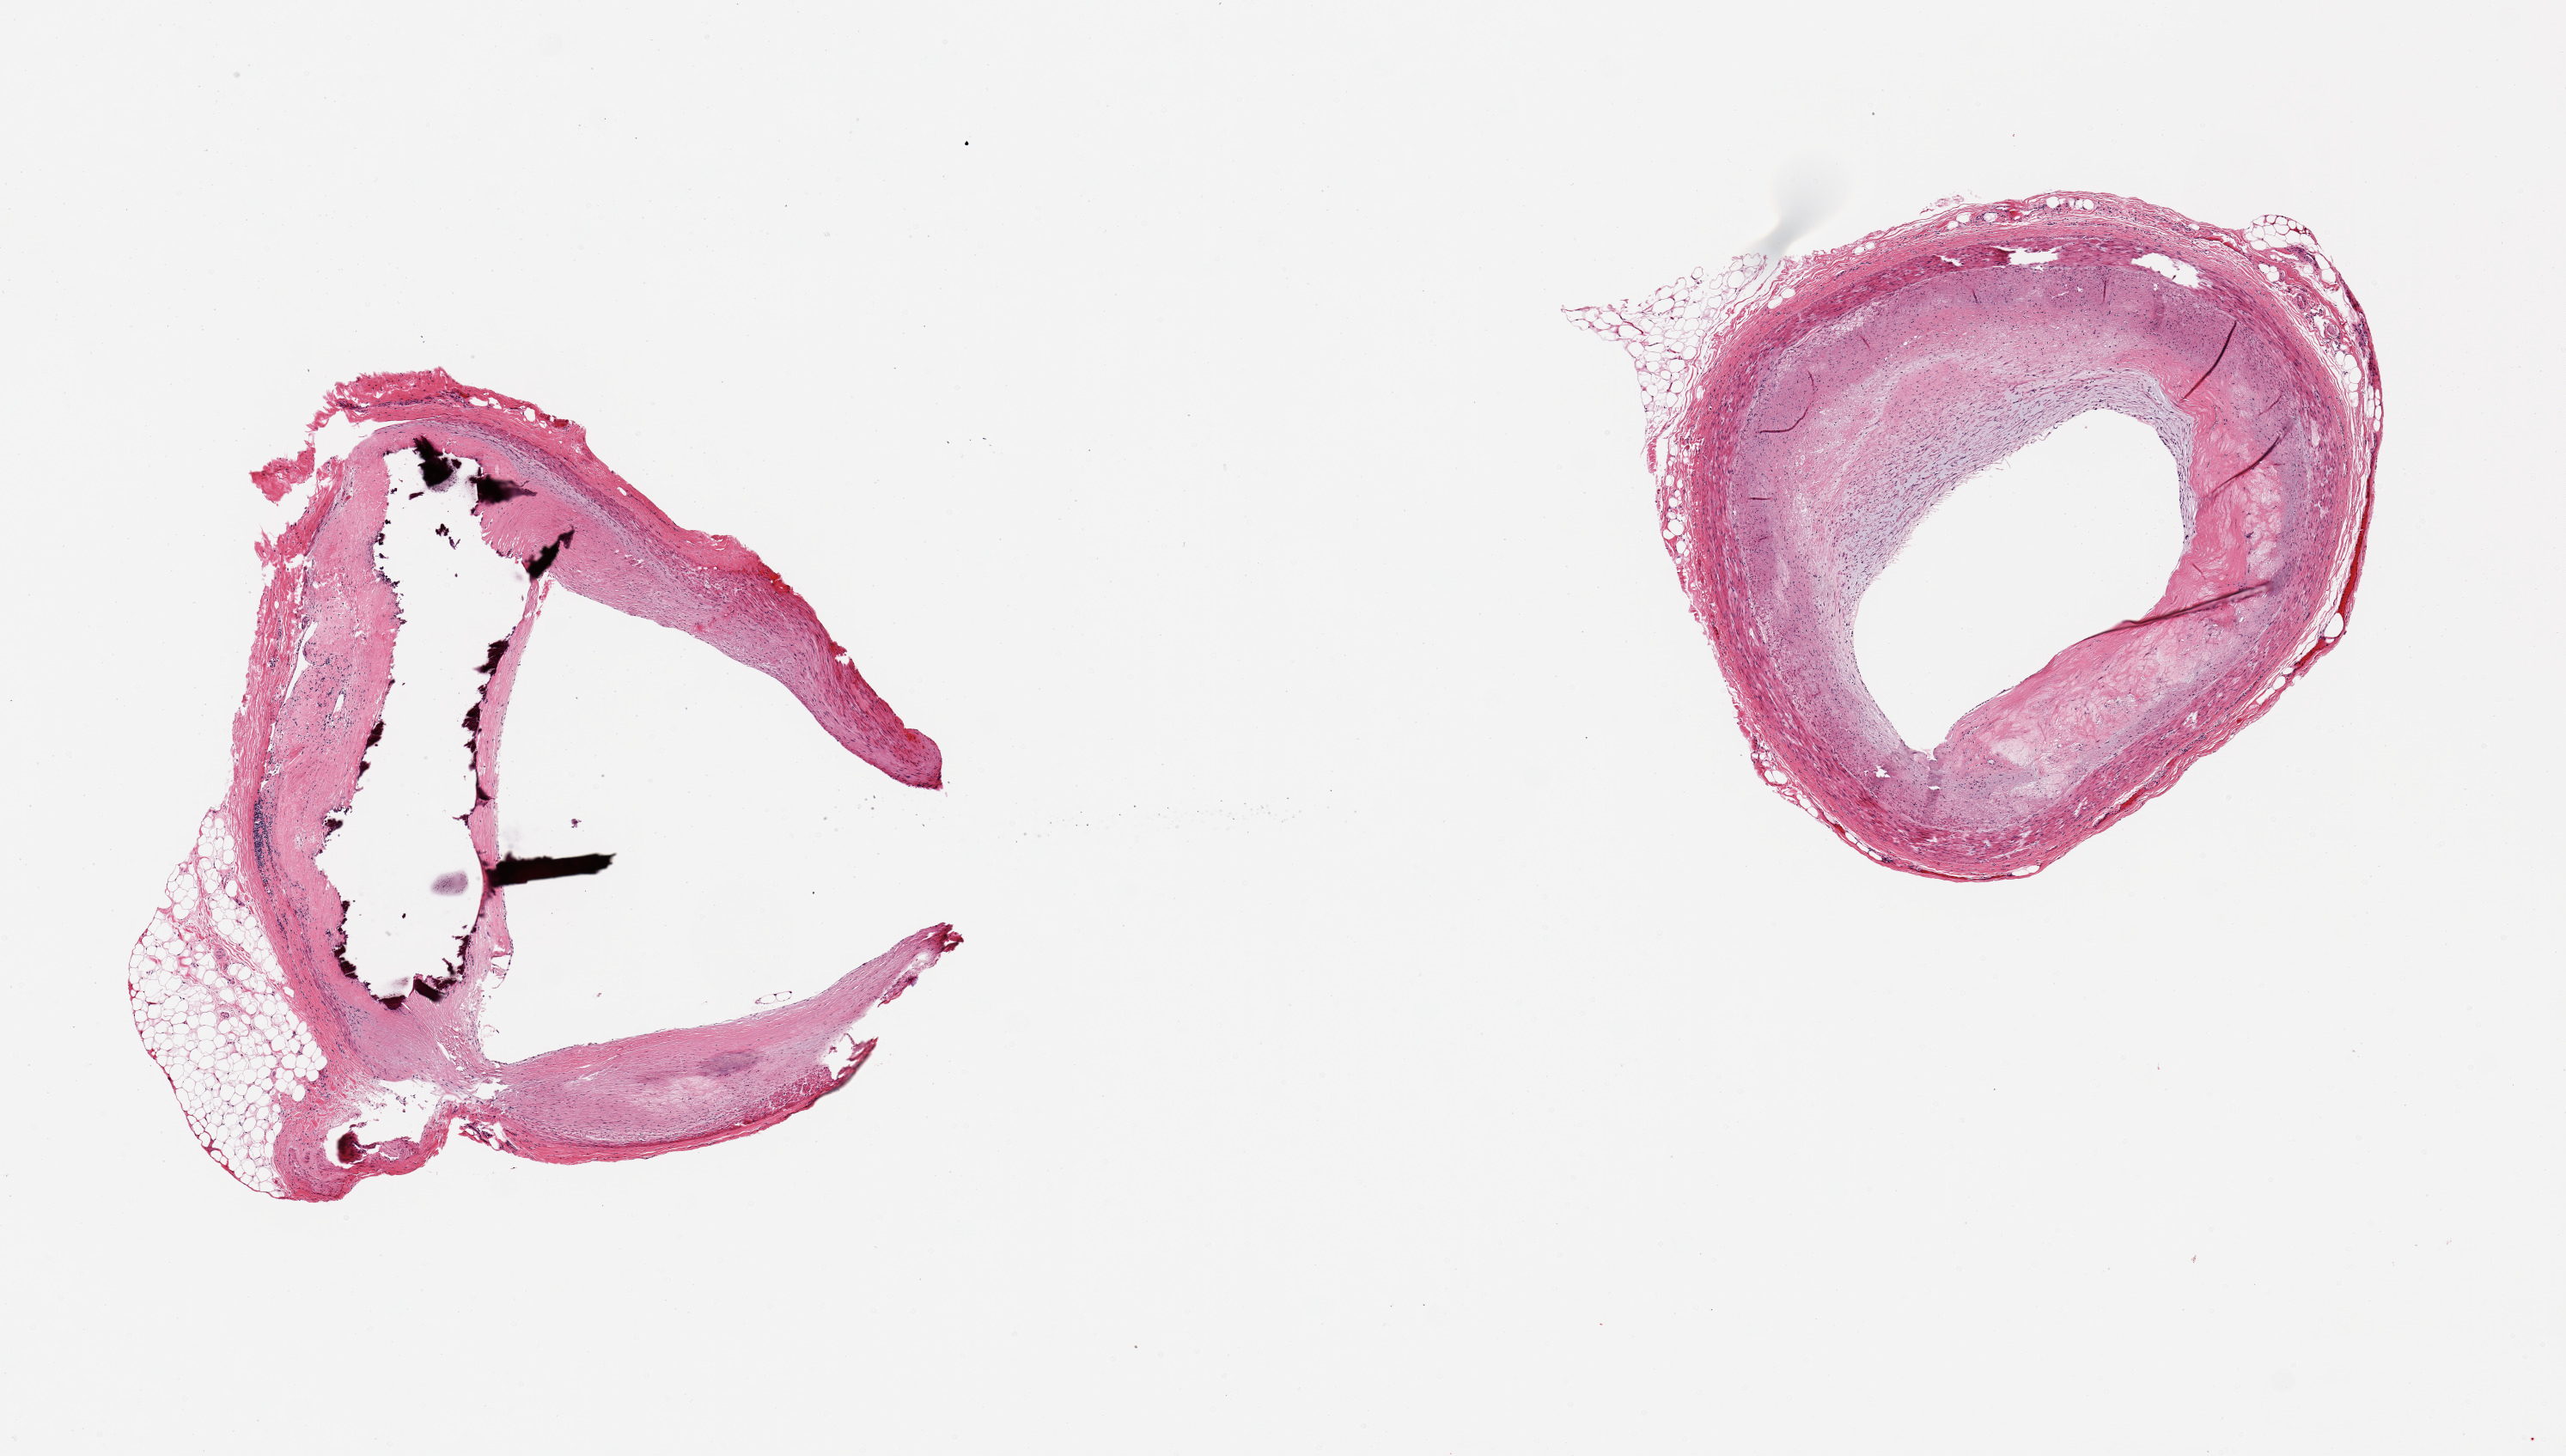
Whole-slide image, haematoxylin and eosin stain, whole scanned area (about 11.8 x 6.7 mm) shown as a low-resolution overview; PAXgene-fixed, paraffin-embedded tissue; target tissue: coronary artery; donor tissue sample. Donor sex: male.
Reviewer comment on this tissue sample: 2 ~3mm d aliquots, ~60% occlusion by atherosclerotis deposits, calcified.